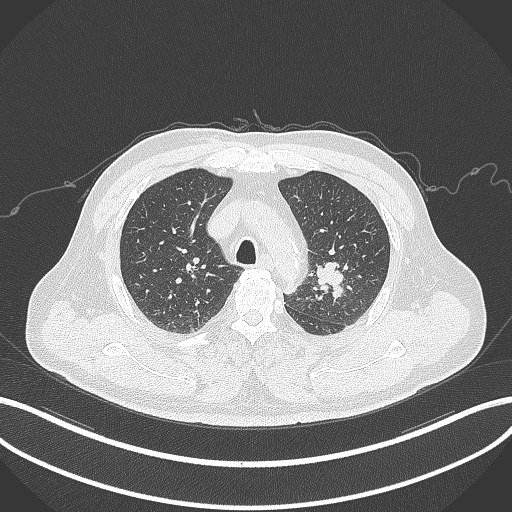
Chest CT, one axial slice; position 231 of 286 along the scan axis; reconstruction kernel B70f; 120 kVp; lung window (W 1500 / L -600 HU); 1 mm slice thickness; 512 × 512 image matrix, field of view 400 × 400 mm. Patient: male, 67 years. From the clinical record (not read from this slice): clinical TNM (as recorded): T2a N1 M0.
Structures marked on this image (bounding box drawn by a radiologist):
- lung tumour (recorded histology: adenocarcinoma): bounding box [x1, y1, x2, y2] px = [313, 259, 344, 296]